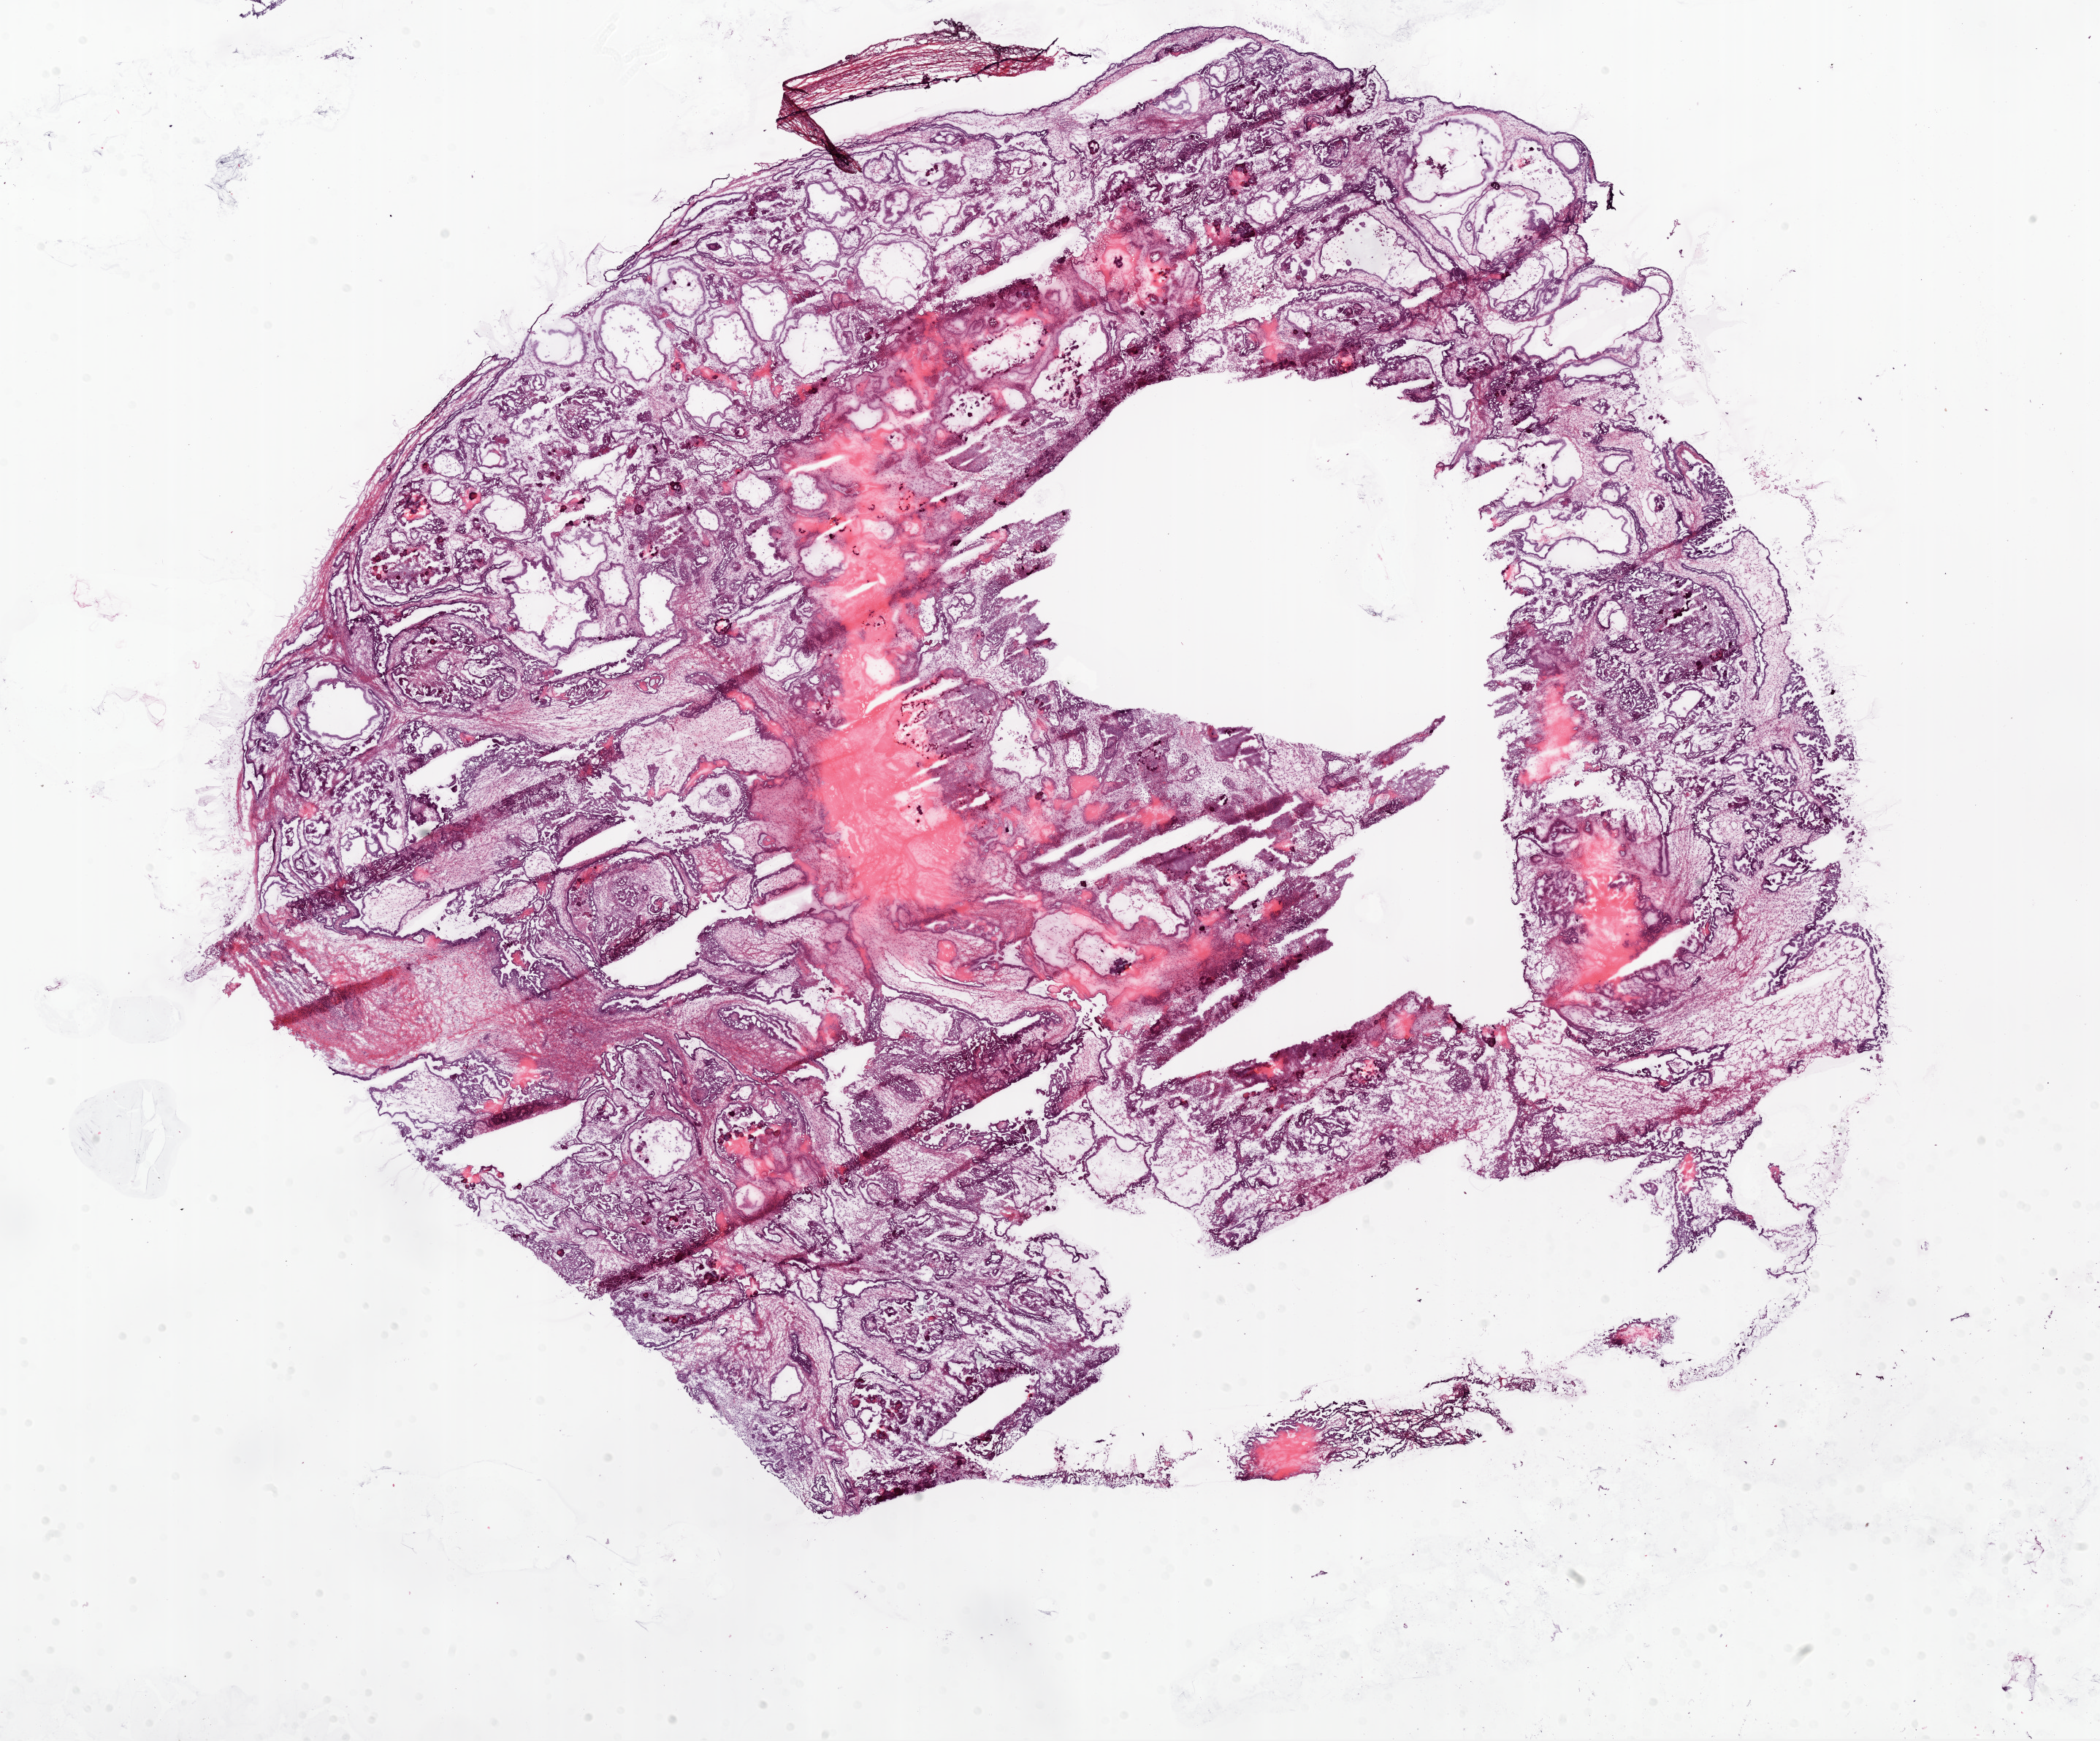
Digitized H&E tissue section (whole slide), whole scanned area (about 23.1 x 19.1 mm, from a 20x scan) shown as a low-resolution overview. Frozen section. Ovary, primary tumour sample. Female patient; age at initial diagnosis 54 years. Histologic grade: G2 (moderately differentiated). Slide review estimates, as recorded: tumour cells 60%, tumour nuclei 80%, normal cells 0%, stromal cells 39%, necrosis 1%.
• pathologic diagnosis: Serous cystadenocarcinoma, NOS
• FIGO stage: IIIC